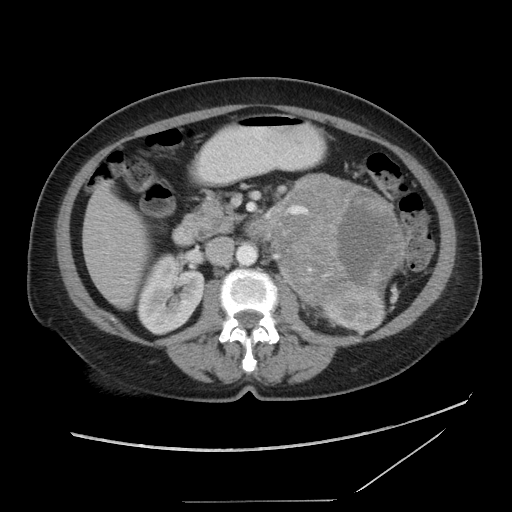
Contrast-enhanced abdominal CT, one axial slice; position 49 of 86 along the scan axis; reconstruction kernel STANDARD; 120 kVp; intravenous contrast given; soft-tissue window (W 400 / L 40 HU); 5 mm slice thickness; 512 × 512 image matrix. Female patient, age 77 years. From the clinical record (not read from this slice): diagnosis: adrenocortical carcinoma; tumour side: left adrenal; tumour size at pathology: 13.1 cm; Ki-67 index: 10 %; stage (as recorded): 3.
Outlined on this slice (semi-automatically segmented with operator editing):
- mass: bounding box <271,173,402,305> (left, top, right, bottom; pixels)